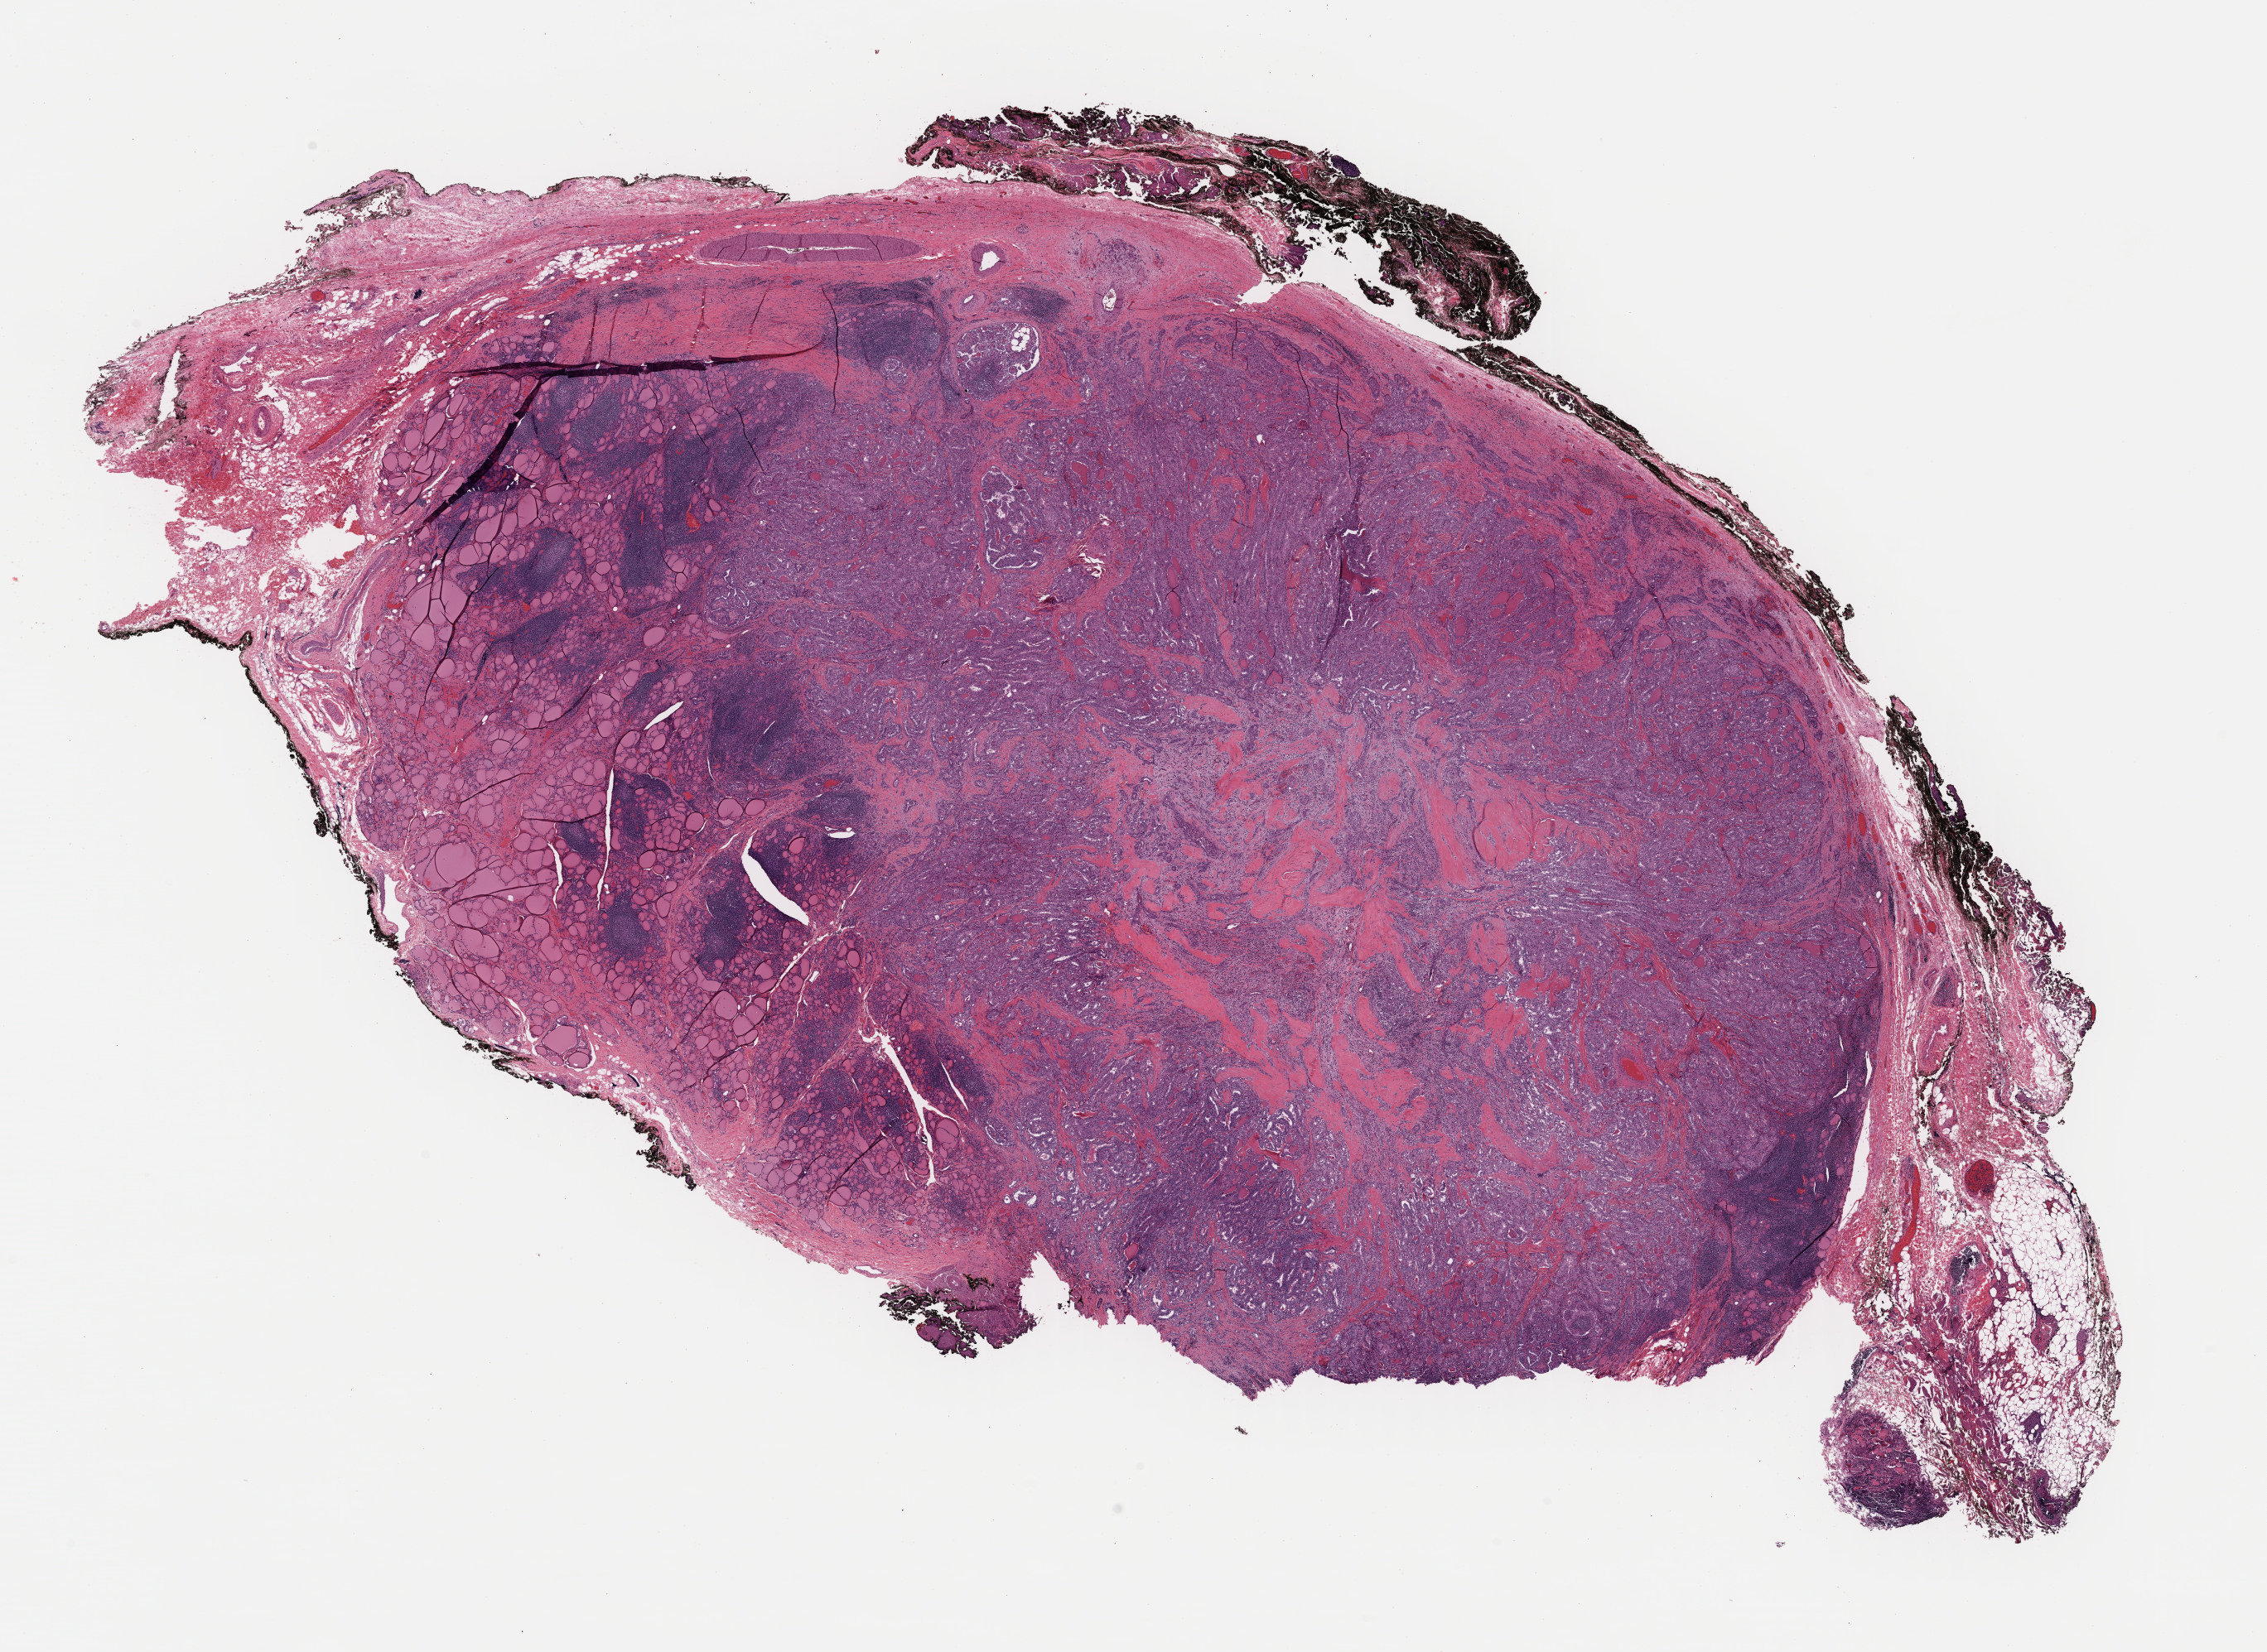
Whole-slide histology image, Hematoxylin and eosin (H&E) stained, a low-resolution overview of the entire scanned area, about 21.6 x 15.7 mm, formalin-fixed paraffin-embedded (FFPE) diagnostic section, primary tumour sample from the thyroid. Patient: male, age at initial diagnosis 47 years.
AJCC pathologic stage: III (7th edition). Diagnosis: Papillary adenocarcinoma, NOS (thyroid gland).